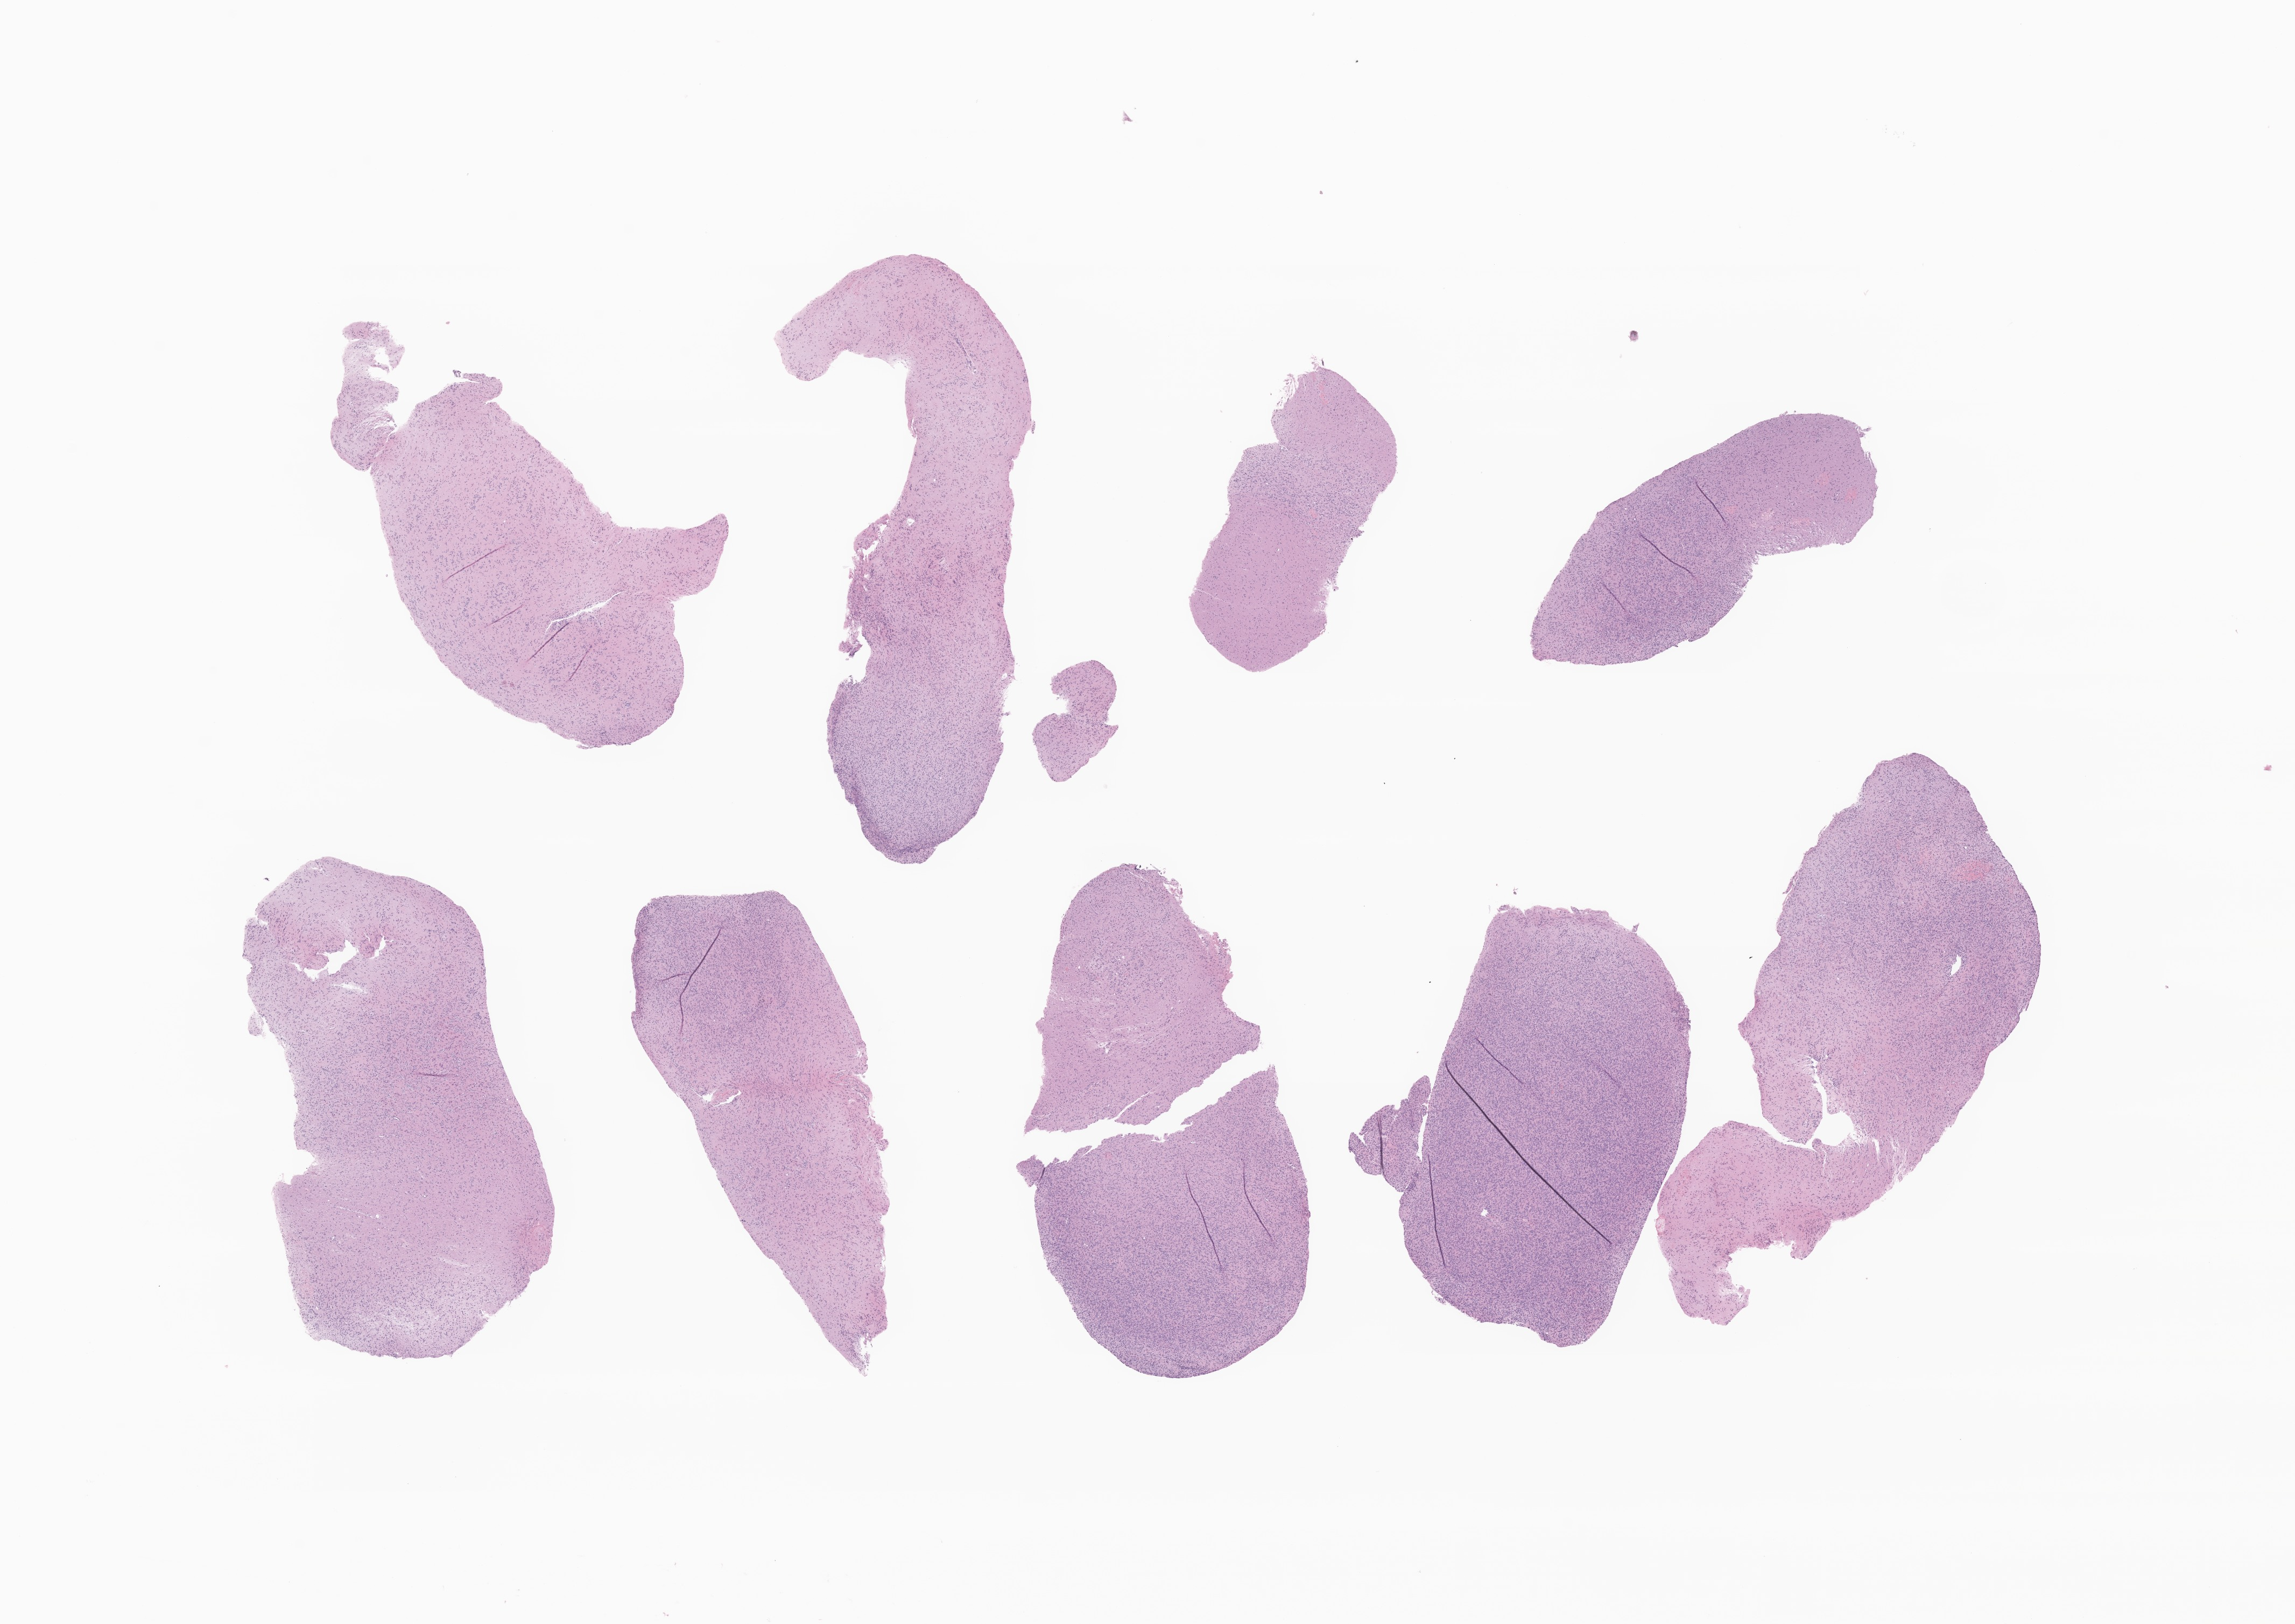
Digitized H&E-stained section of tumor tissue from the brain, whole scanned area (about 18.0 x 12.7 mm) shown as a low-resolution overview, formalin-fixed, paraffin-embedded (FFPE) tissue. Male patient, age 56 months (4 years 8 months).
Diagnosis: Neoplasm, uncertain whether benign or malignant.